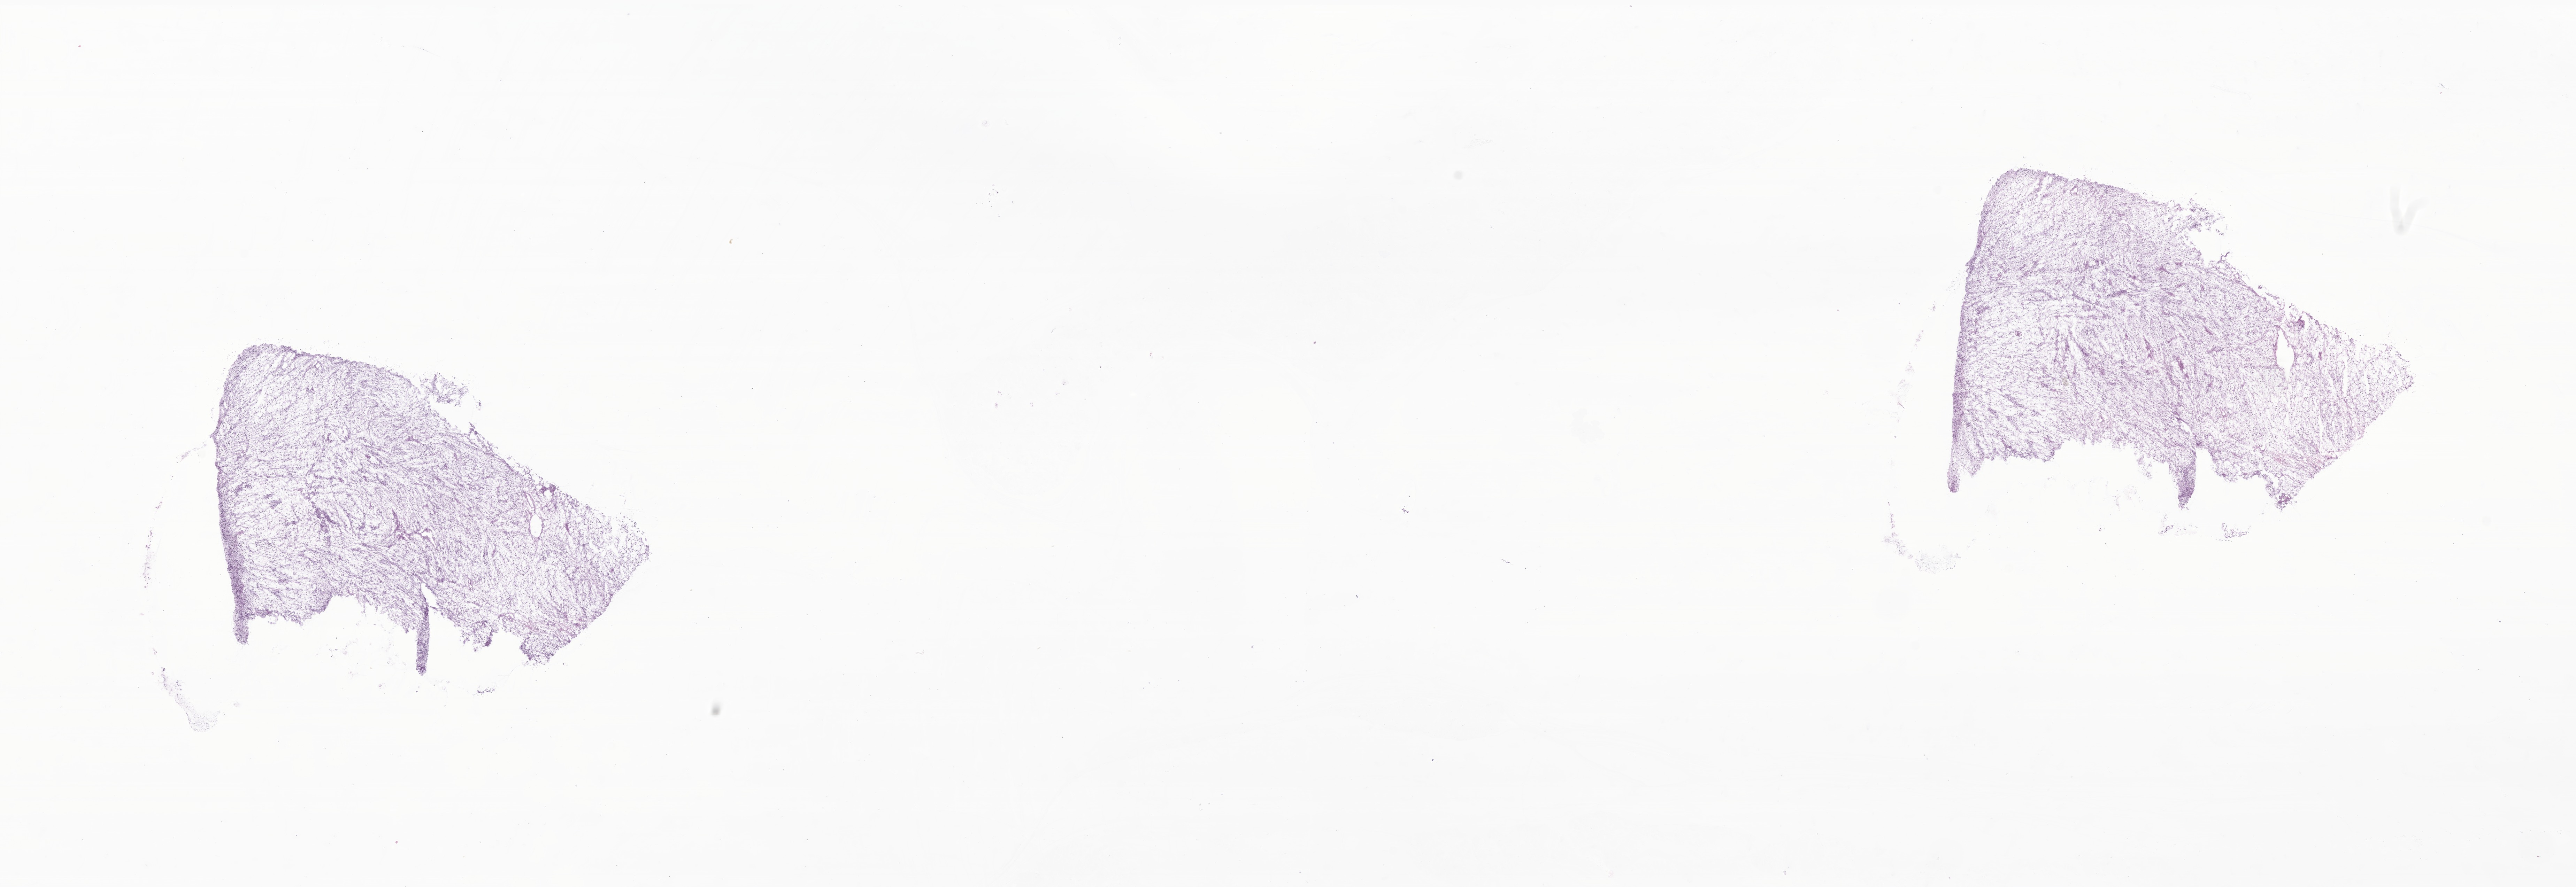
Whole-slide image, hematoxylin and eosin (H&E) stain of tumor tissue from the soft tissue, a low-resolution overview of the entire scanned area, about 31.2 x 10.7 mm. Frozen section. Male patient, age 196 months (16 years 4 months).
Diagnosis: Embryonal rhabdomyosarcoma, NOS.